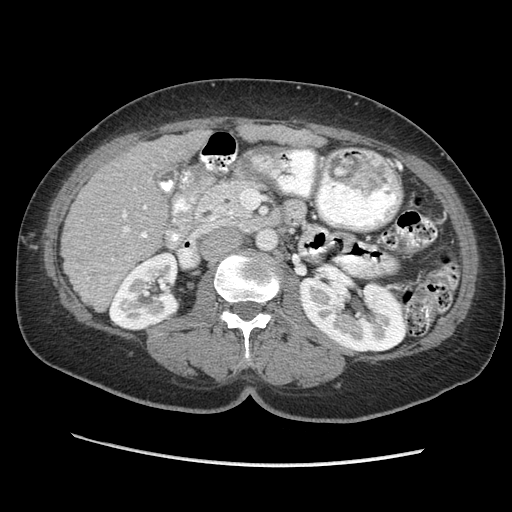
Contrast-enhanced abdominal CT (liver protocol), one axial slice. Position 110 of 170 along the scan axis. 140 kVp. Soft-tissue window (W 400 / L 40 HU). 2.5 mm slice thickness. 512 × 512 image matrix. From the clinical record (not read from this slice): diagnosis: hepatocellular carcinoma (patient treated with transarterial chemoembolisation; whether this scan precedes or follows treatment is not stated here); TNM stage (as recorded): Stage-II; Child-Pugh class: A; tumour differentiation: no biopsy; tumour nodularity: multinodular.
Outlined on this slice (semi-automatic segmentation, software-assisted and operator-edited):
- liver parenchyma outside the tumour (the mass and vessels are separate outlines, so this box may not span the whole liver): bounding box [x1, y1, x2, y2] px = [62, 130, 210, 310]
- liver vessels: [123, 188, 147, 238]